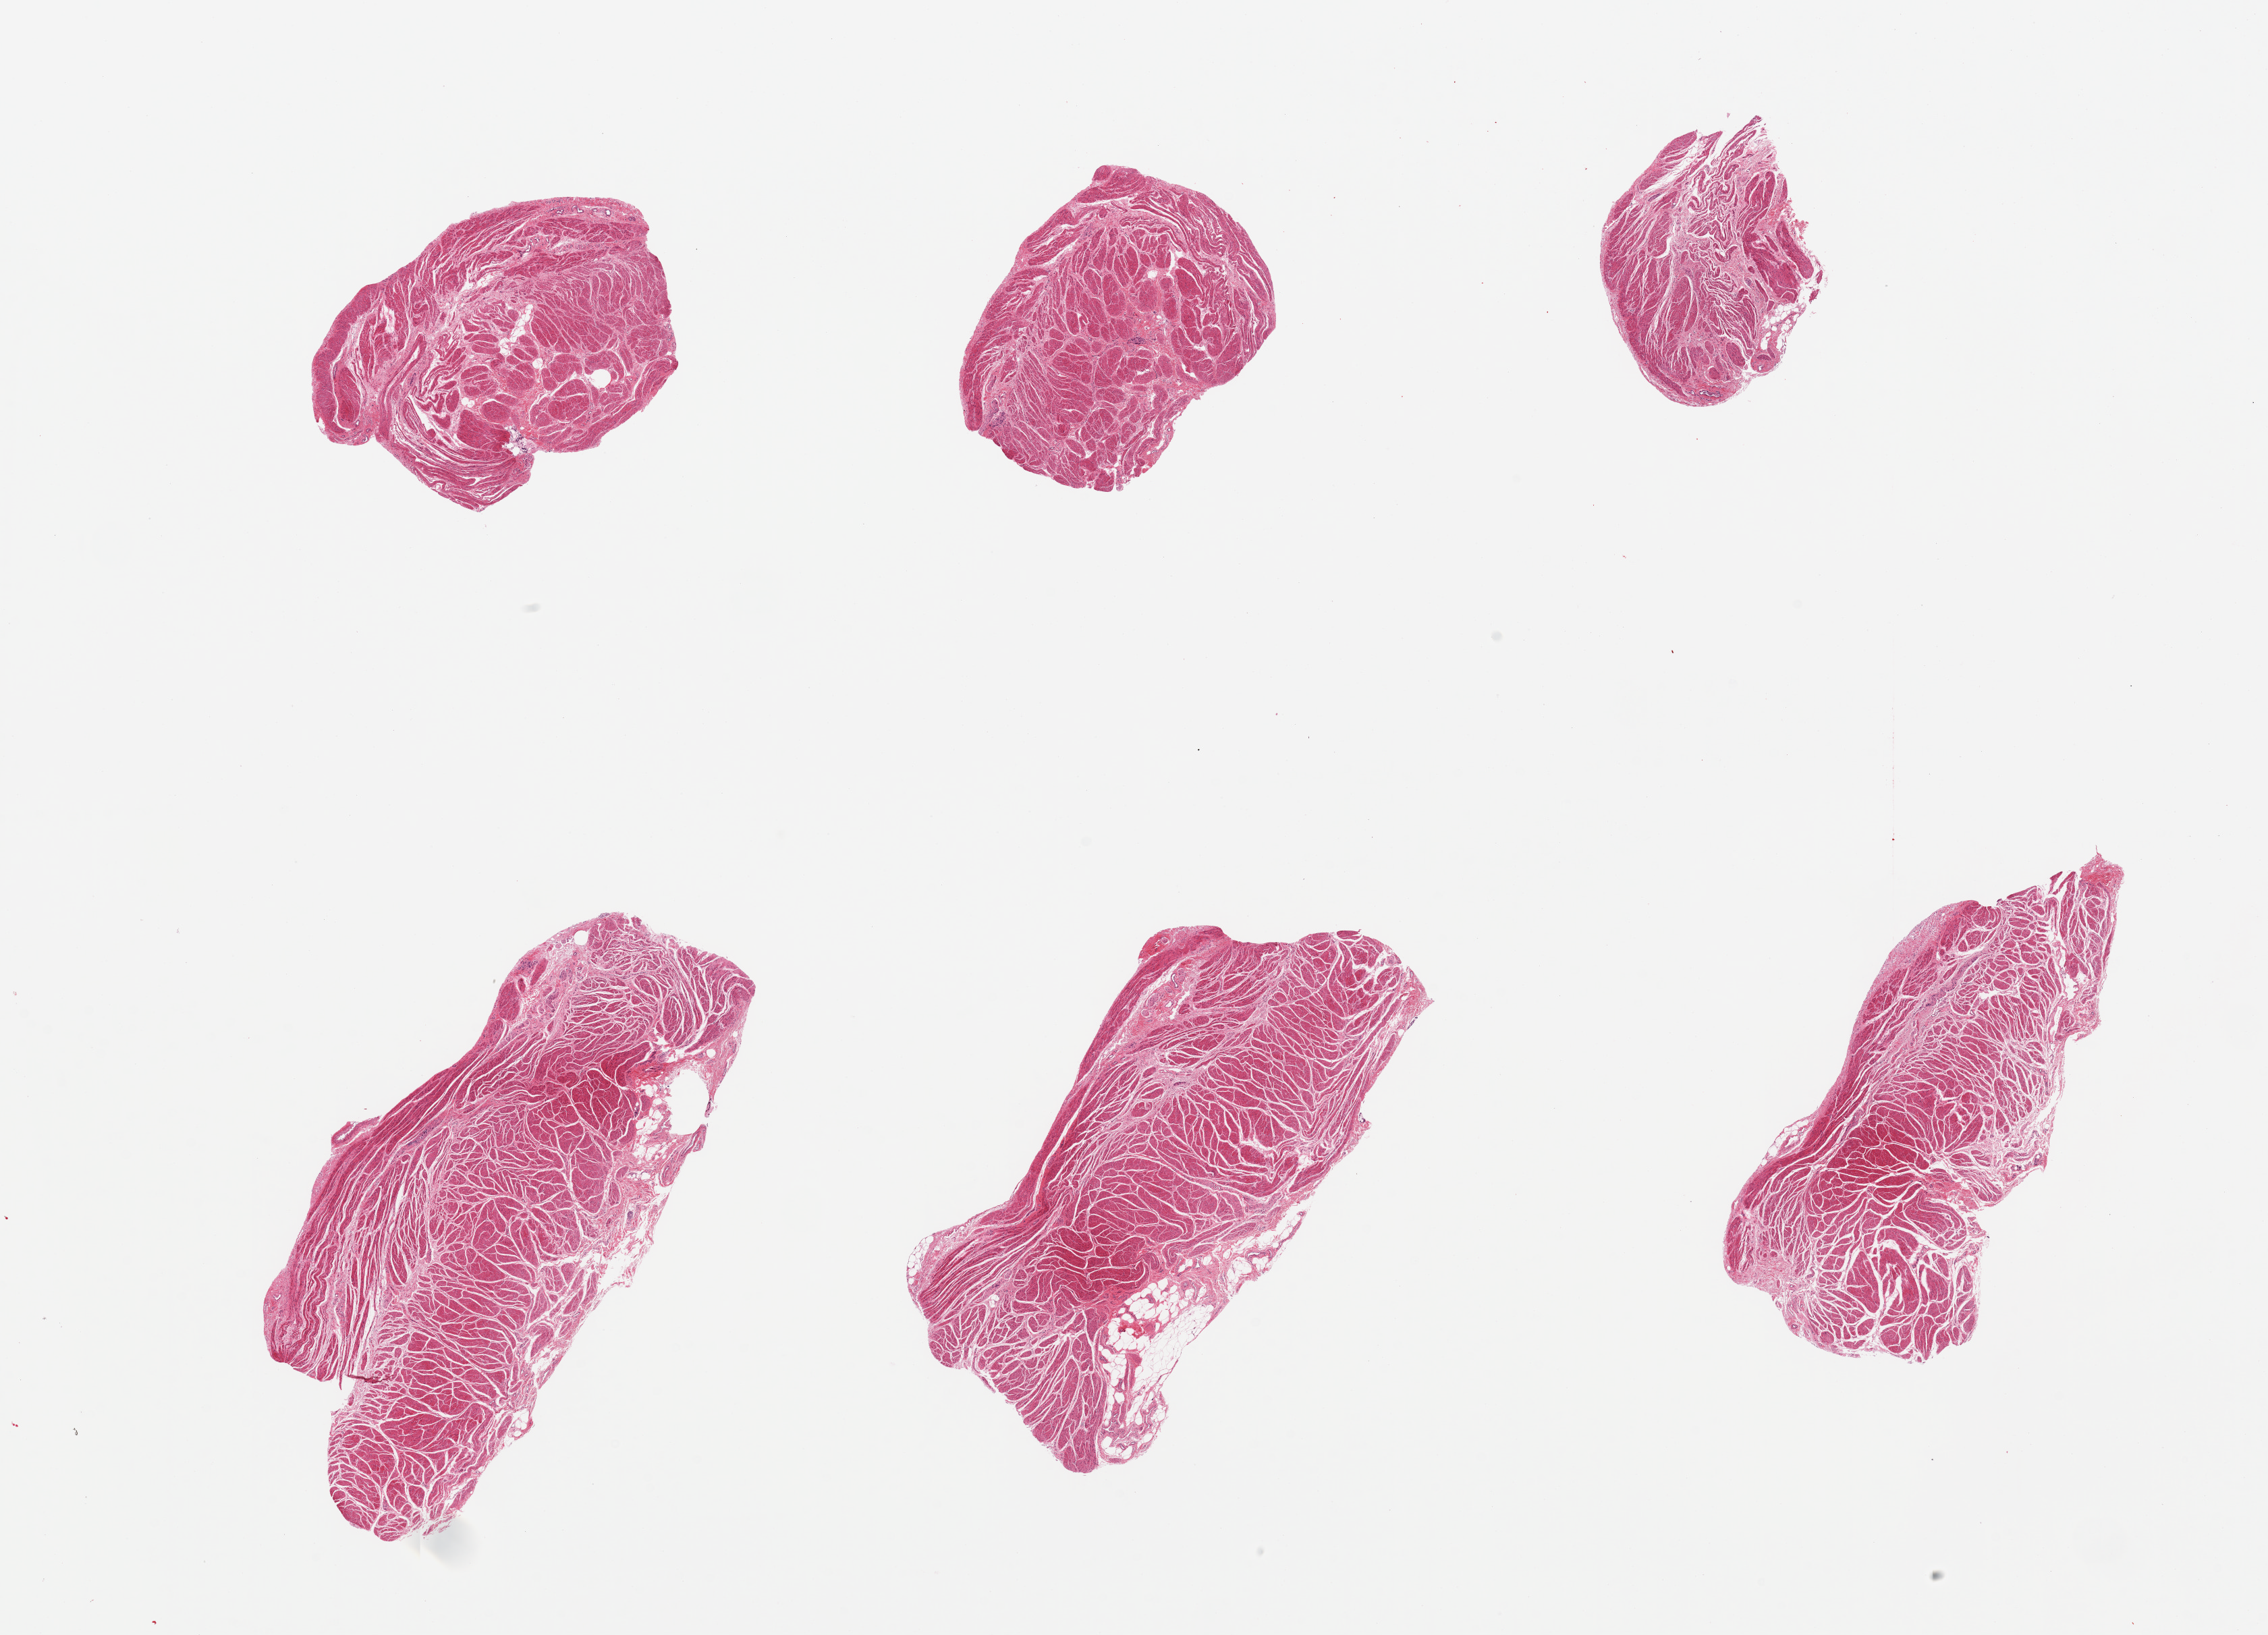
H&E whole-slide image — a low-resolution overview of the entire scanned area, about 26.6 x 19.2 mm (from a 20x scan), PAXgene-fixed paraffin-embedded (PFPE) section, target tissue: gastroesophageal junction, tissue donor sample. Female donor.
Review note (as recorded): 6 pieces, well trimmed.